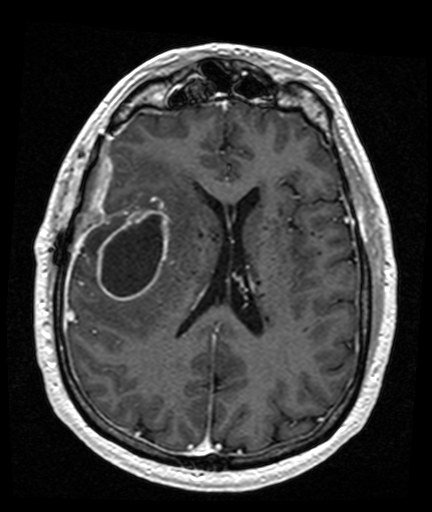
Brain MRI from a brain-tumour surgery series, one axial slice; slice 69 of 176 in the series (ordered by position); T1-weighted post-contrast; 1 mm slice thickness; 432 × 512 image matrix. Case-level facts recorded for this patient, not image findings: histopathology: Glioblastoma; WHO grade: 4; IDH mutation: no.
Outlined on this slice (expert manual segmentation):
- tumour: box from (x=97, y=207) to (x=171, y=301) px